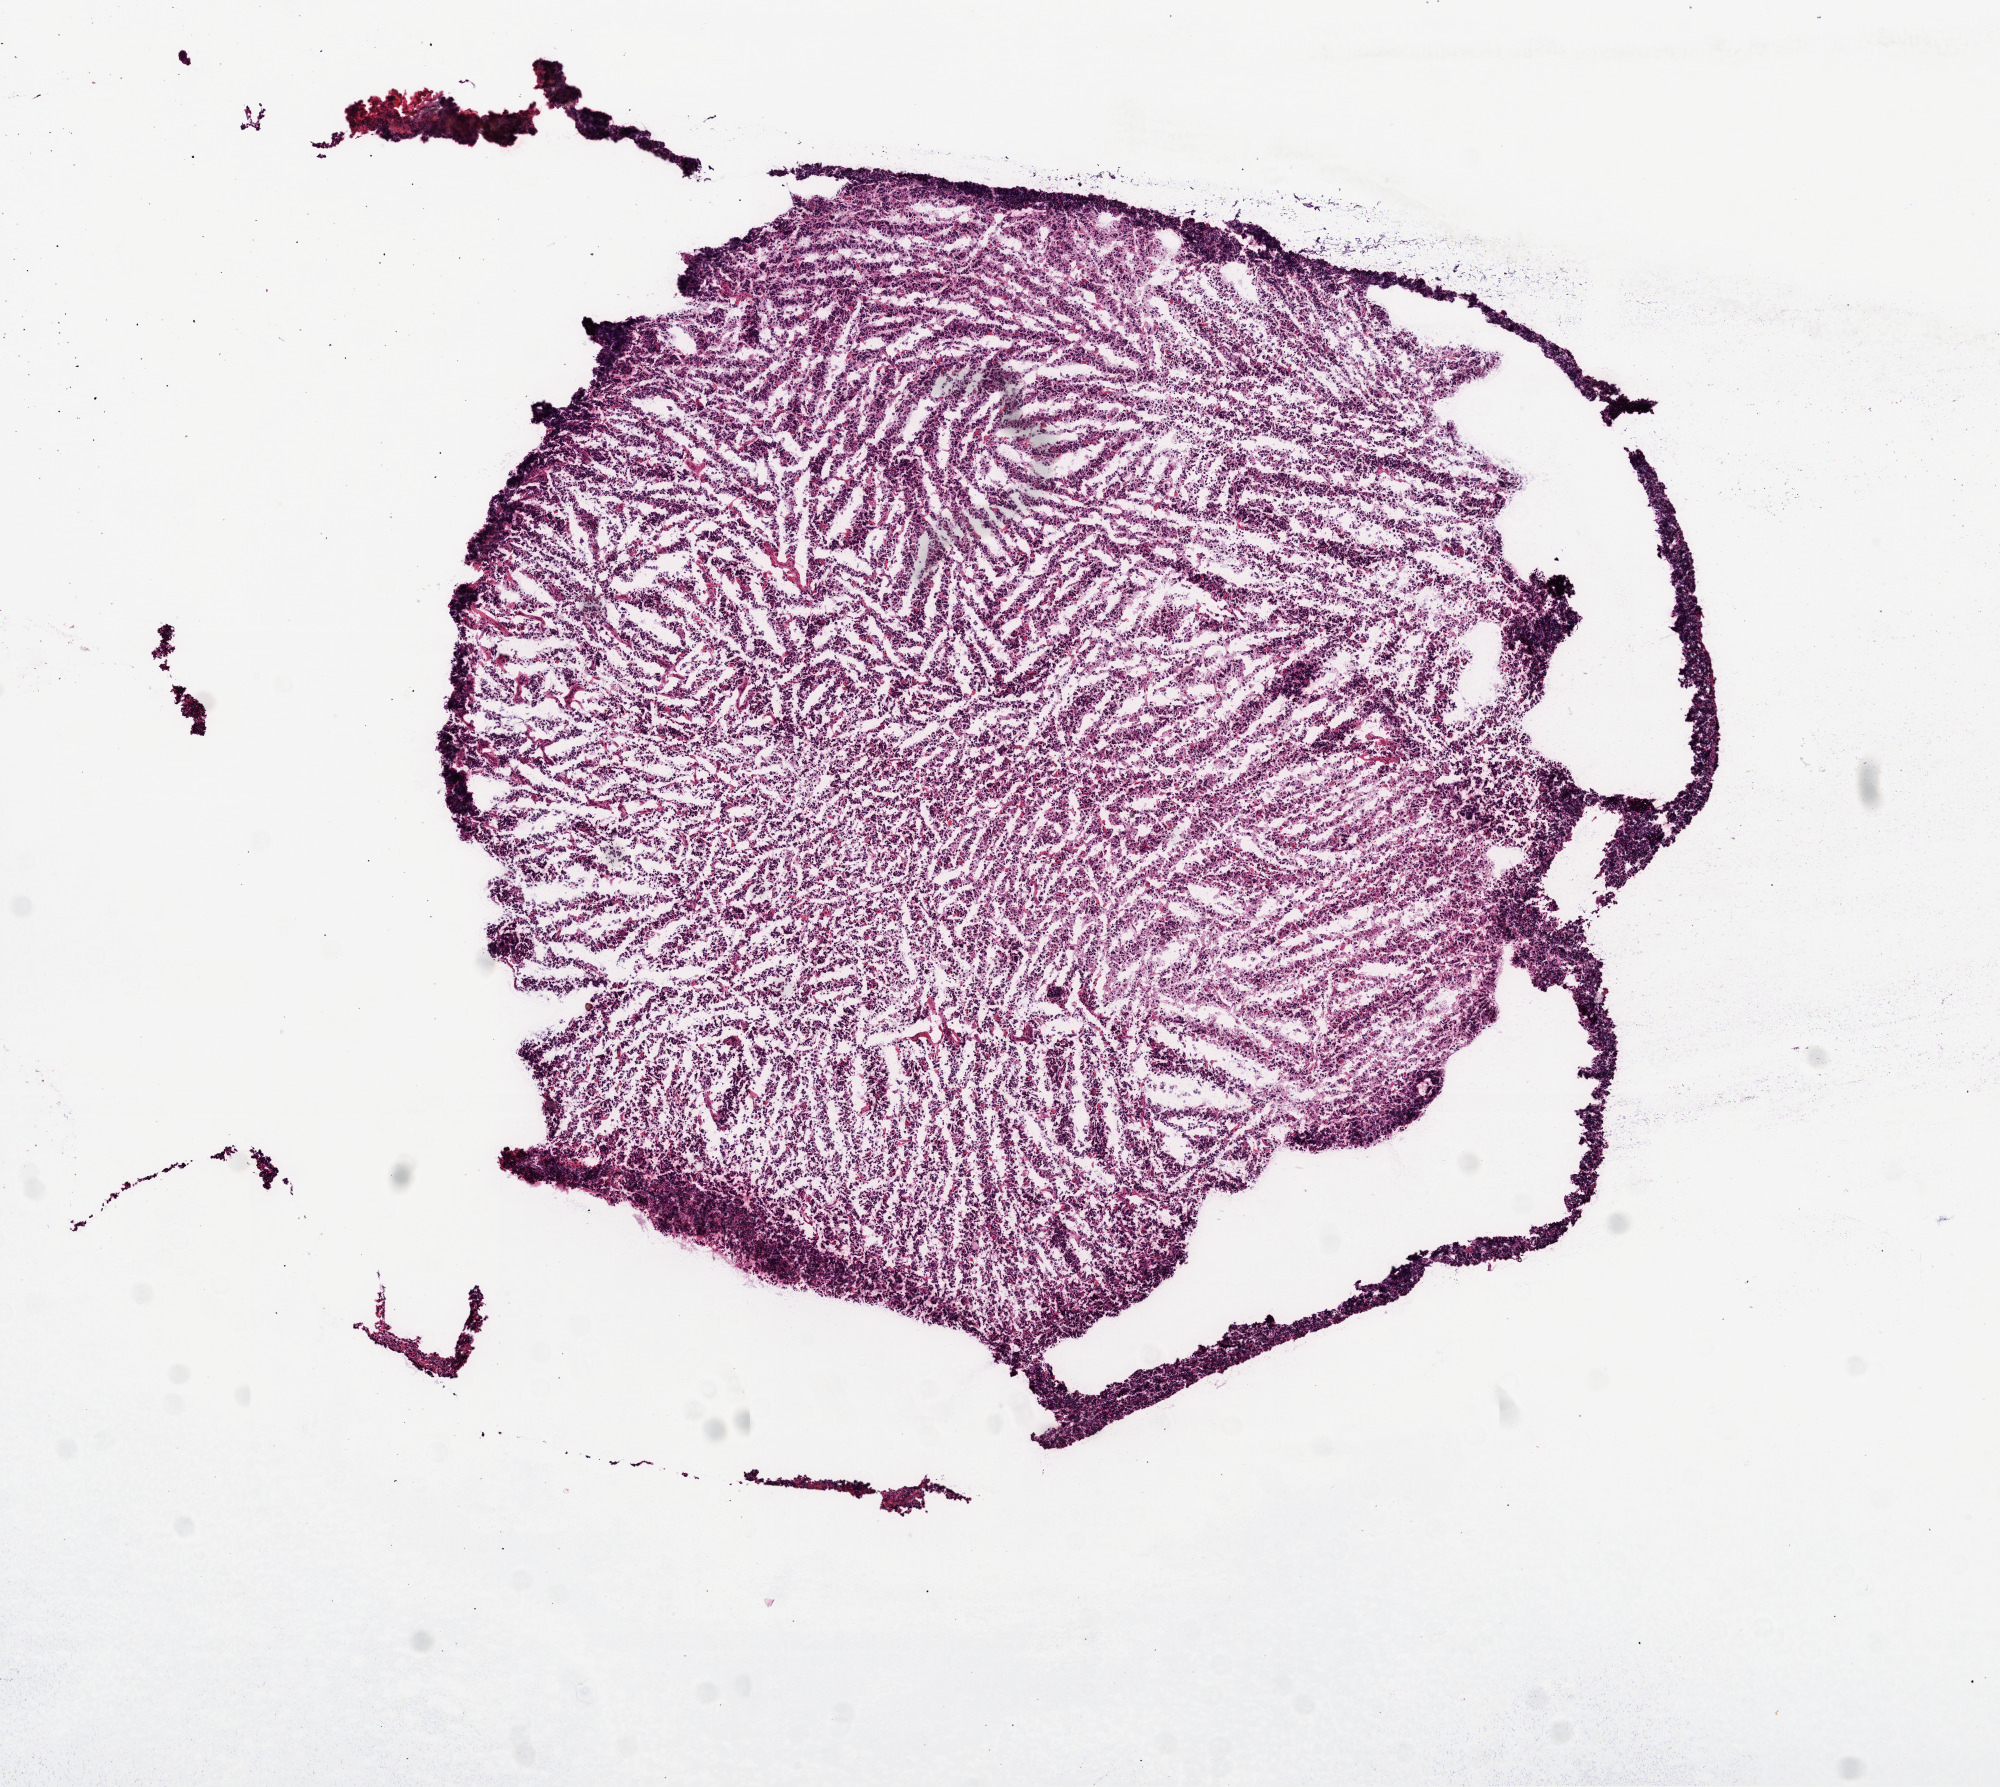
Digitized Hematoxylin and eosin (H&E) stained tissue section (whole slide), a low-resolution overview of the entire scanned area, about 8.0 x 7.2 mm (acquisition: 20x scan), frozen section, sample: primary tumour, brain. Male patient; age at initial diagnosis 40 years.
Diagnosis: Glioblastoma.